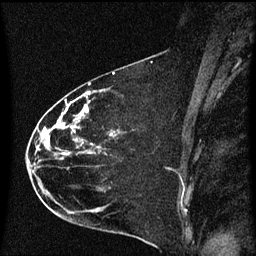
Breast MRI (dynamic contrast-enhanced), one sagittal slice. Position 35 of 60 along the scan axis. Dynamic contrast-enhanced series, image 2 of 3 at this slice position (ordered by acquisition). 1.5 T. TE 4.2 ms, TR 8.4 ms. 256 × 256 image matrix, field of view 200 × 200 mm. Patient: female, 35 years. From the clinical record (not read from this slice): setting: breast cancer imaged before/during neoadjuvant chemotherapy; receptor status: HER2-positive.
Annotated regions visible in this slice (semi-automatically segmented with operator editing):
- analysis volume of interest (the breast-tissue region the enhancement analysis was run in; not a lesion): bounding box <27,68,174,173> (left, top, right, bottom; pixels)
- tumour enhancement mask (voxels above the 70 % enhancement threshold inside the analysis volume of interest): <41,92,113,155>